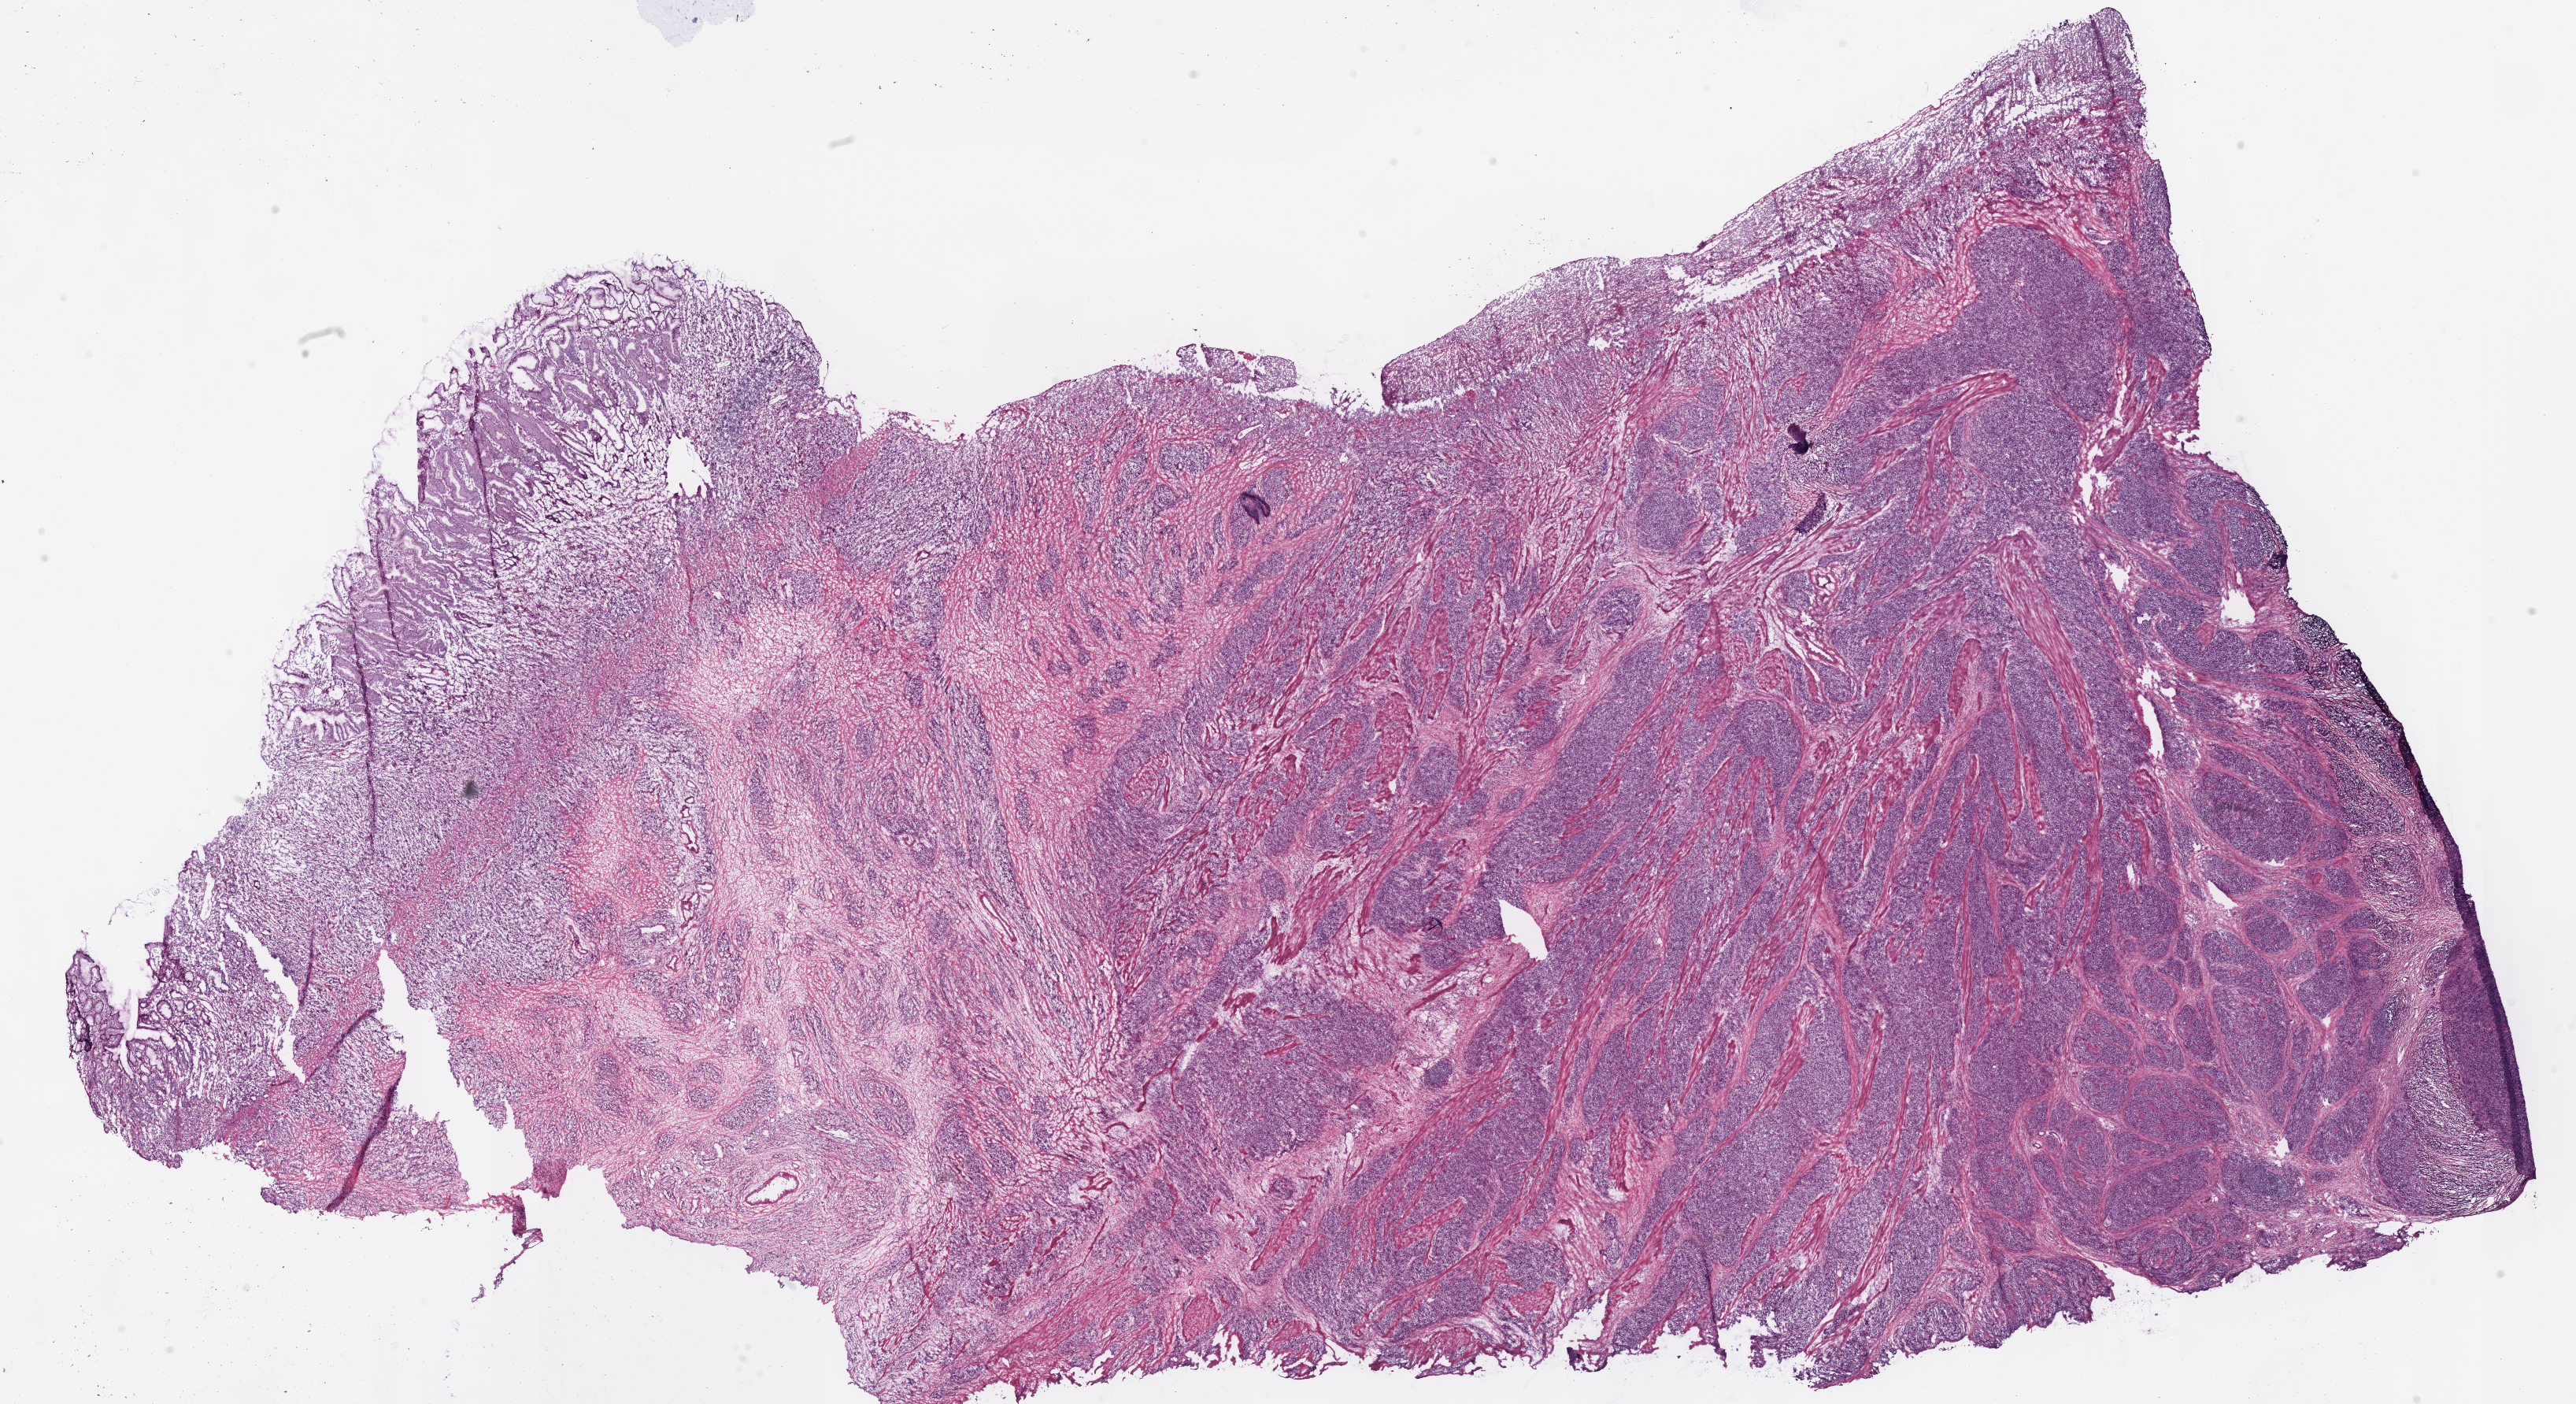
H&E-stained whole-slide image — shown as a low-resolution overview of the whole scanned area (about 25.8 x 14.0 mm, from a 40x scan). Frozen section from the bottom of the tissue portion. Stomach, primary tumour sample. Male patient; age at initial diagnosis 55 years. Pathologist review of this section (percent, as recorded): tumour cells 75%, tumour nuclei 80%.
Pathologic diagnosis: Adenocarcinoma, NOS (fundus of stomach).